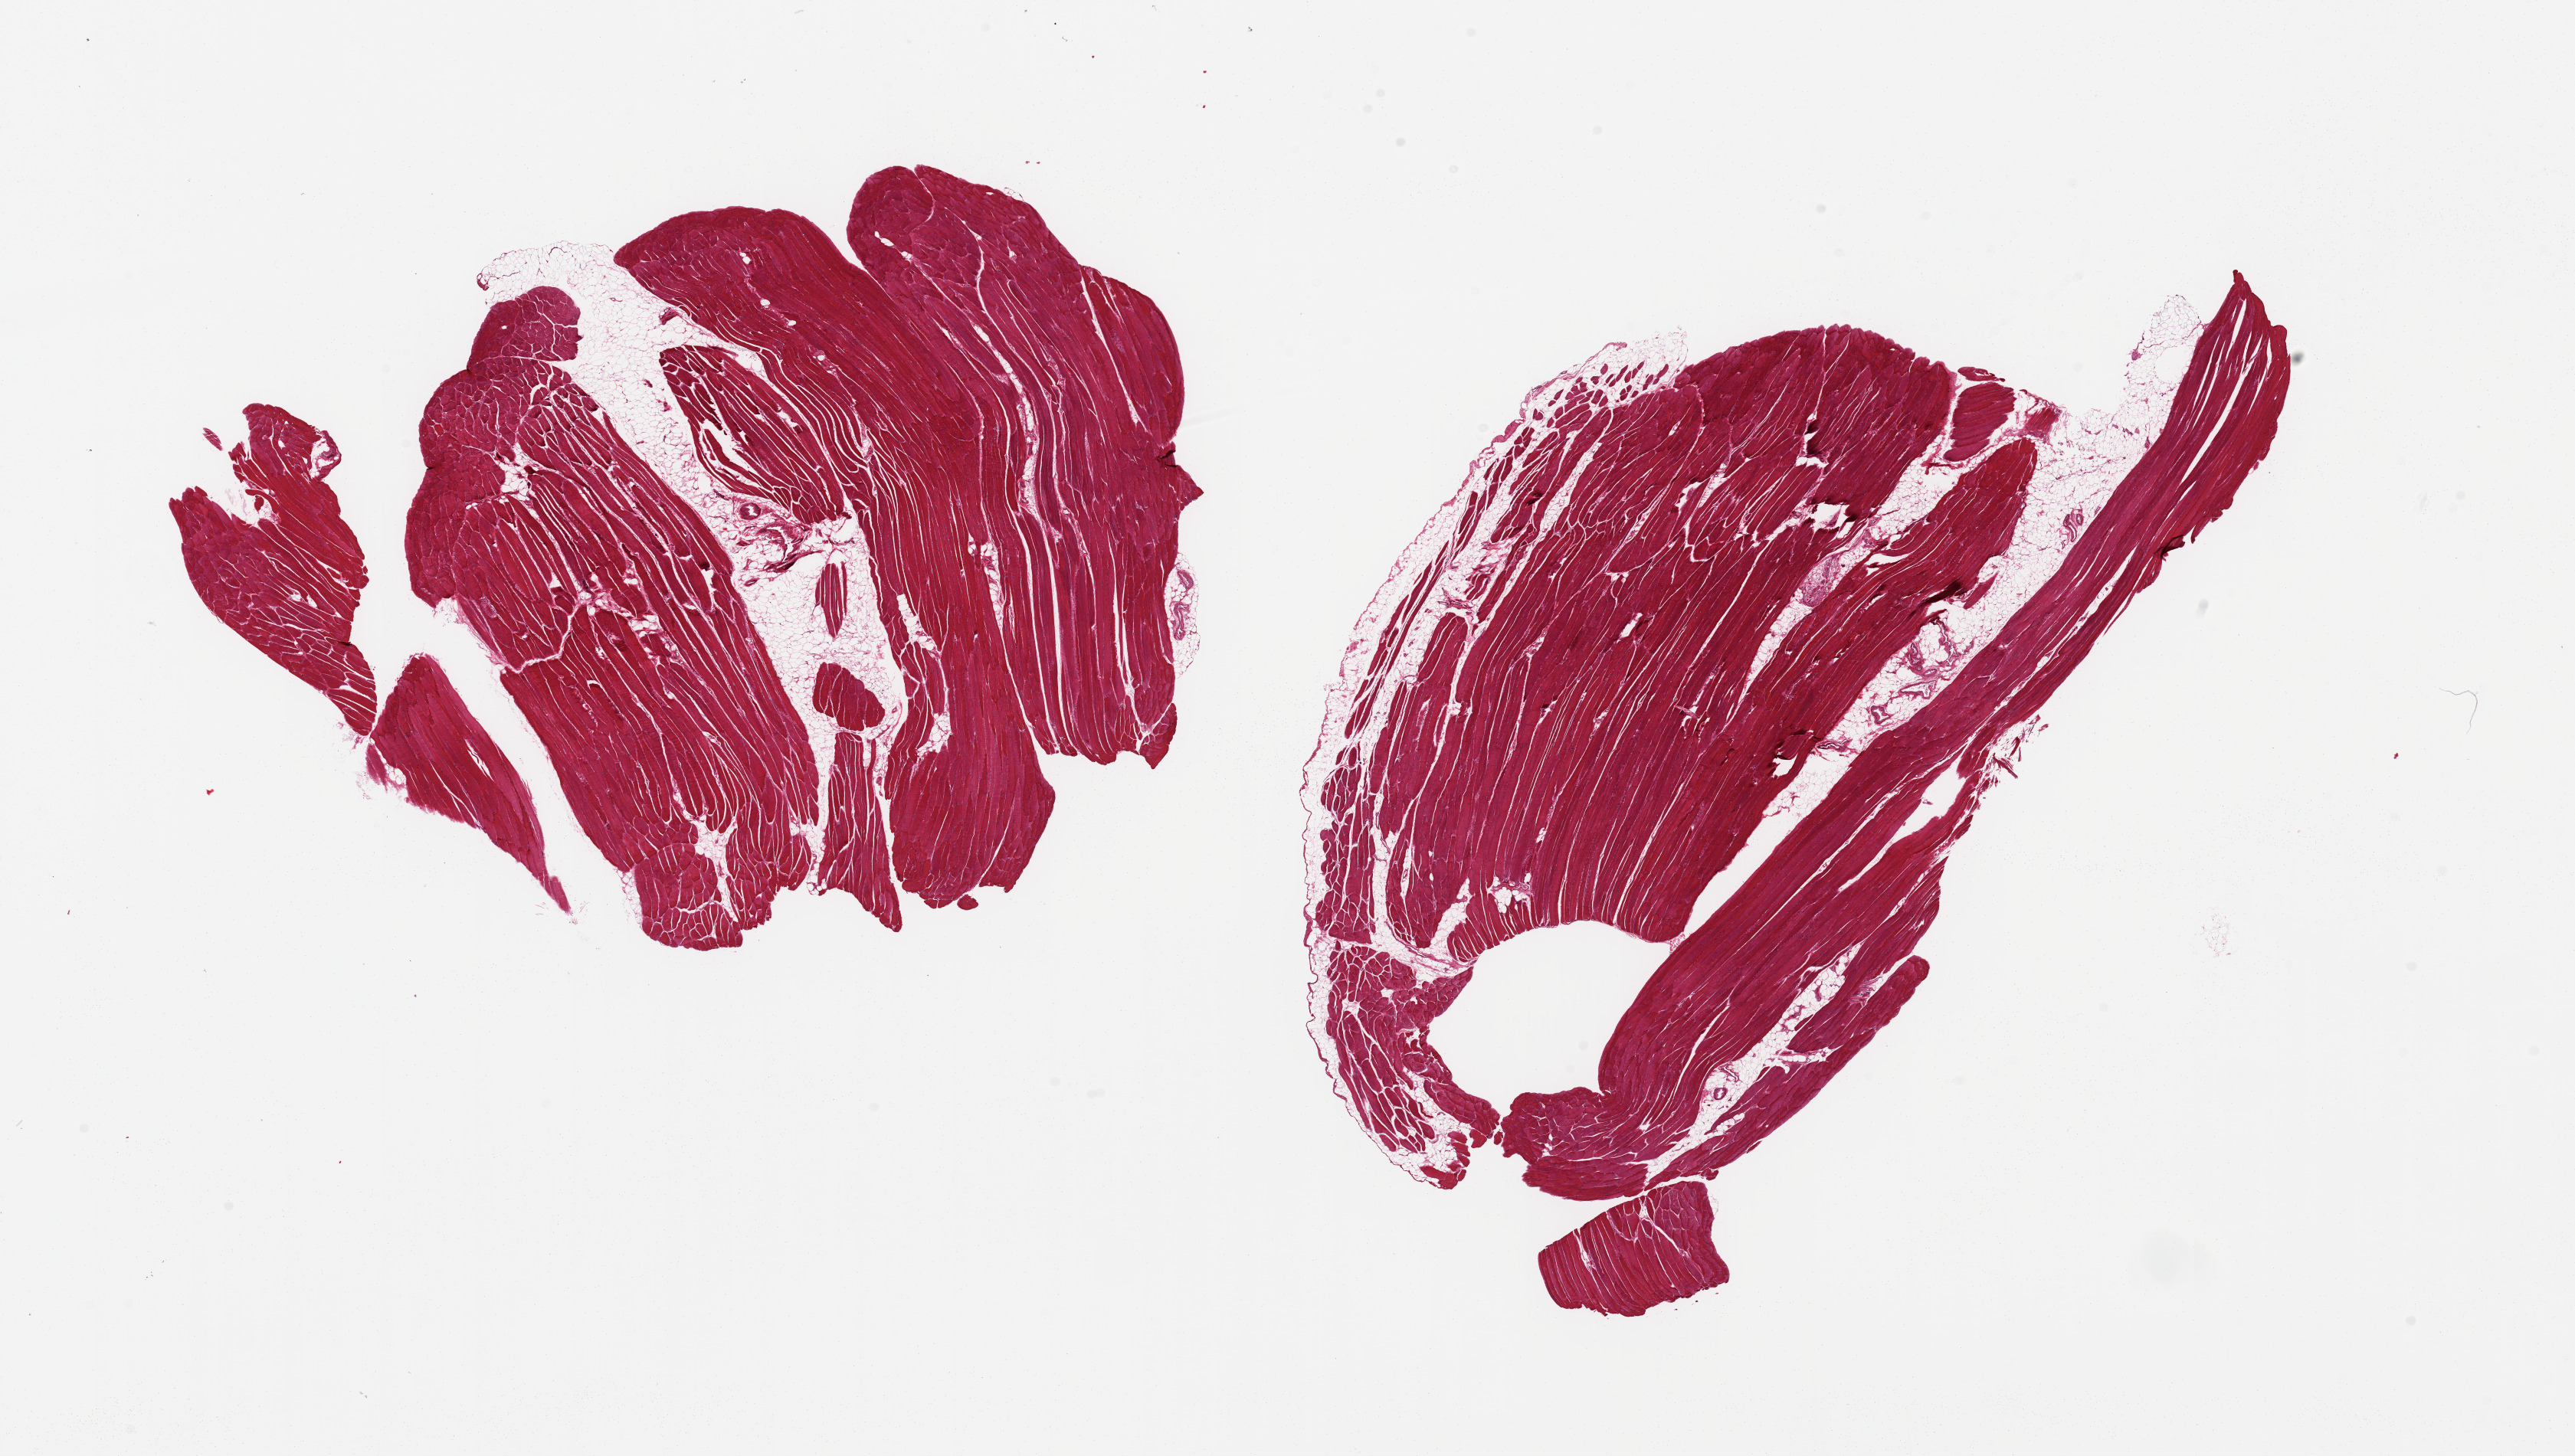
Whole-slide image, haematoxylin and eosin stain — shown as a low-resolution overview of the whole scanned area (about 26.6 x 15.0 mm), PAXgene-fixed paraffin-embedded (PFPE) section, sampled site (target tissue): skeletal muscle, tissue donor sample. Donor: male.
Reviewer comment on this tissue sample: 2 pieces; skeletal muscle with 10 and 15% fat.